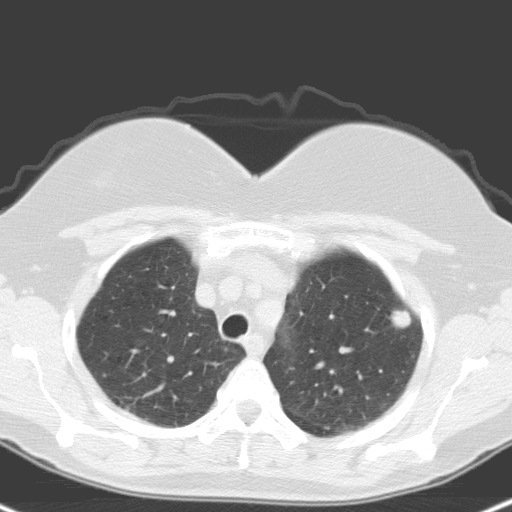
Chest CT (low-dose screening protocol), one axial image; first (baseline) screen; lung window (W 1500 / L -600 HU); 3.2 mm slice thickness. Female, age 59 years at enrolment. Current smoker at enrolment.
Lesion marked by an expert reader, box from (x=382, y=297) to (x=424, y=342) px. The screening reader recorded 2 non-calcified nodules or masses ≥4 mm on this exam (right upper lobe, left upper lobe); which of them this box marks is not recorded. Participant outcome: lung cancer diagnosed 48 days after this screen — large cell neuroendocrine carcinoma, left upper lobe, poorly differentiated (G3), stage IA (AJCC 6th edition), 12 mm at pathology.